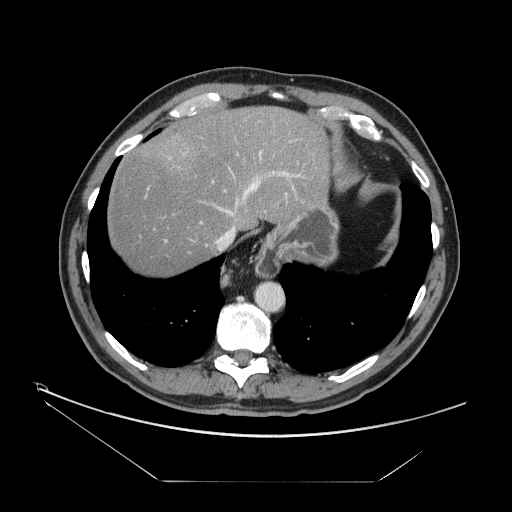
Contrast-enhanced abdominal CT, one axial slice; slice 133 of 161 in the series (ordered by position); reconstruction kernel STANDARD; intravenous contrast given; soft-tissue window (W 400 / L 40 HU); 2.5 mm slice thickness; 512 × 512 image matrix, field of view 440 × 440 mm. Male patient, age 65 years. From the clinical record (not read from this slice): diagnosis: colorectal cancer liver metastases, imaged before liver resection.
Structures marked on this image (expert manual segmentation):
- hepatic veins: bounding box [x1, y1, x2, y2] px = [205, 172, 289, 251]
- liver: [107, 106, 328, 275]
- planned liver remnant (the part of the liver to remain after resection): [106, 106, 328, 275]
- portal vein (with intrahepatic branches): [147, 115, 298, 243]